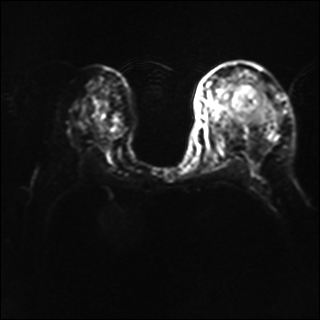
Breast MRI, one axial slice; position 22 of 40 along the scan axis; diffusion-weighted series; image 2 of 4 stored at this slice position (different b-values; order by instance number); 1.5 T; 4 mm slice thickness; 320 × 320 image matrix. Female patient.
Outlined on this slice (outlined manually by an expert reader):
- tumour on diffusion-weighted imaging: box from (x=236, y=83) to (x=261, y=107) px